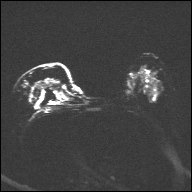
Breast MRI, one axial slice. Slice 20 of 32 in the series (ordered by position). Diffusion-weighted series; image 2 of 4 stored at this slice position (different b-values; order by instance number). 1.5 T. 192 × 192 image matrix, field of view 360 × 360 mm. Female patient.
Annotated regions visible in this slice (manually delineated by an expert):
- tumour on diffusion-weighted imaging: bounding box <37,80,60,87> (left, top, right, bottom; pixels)